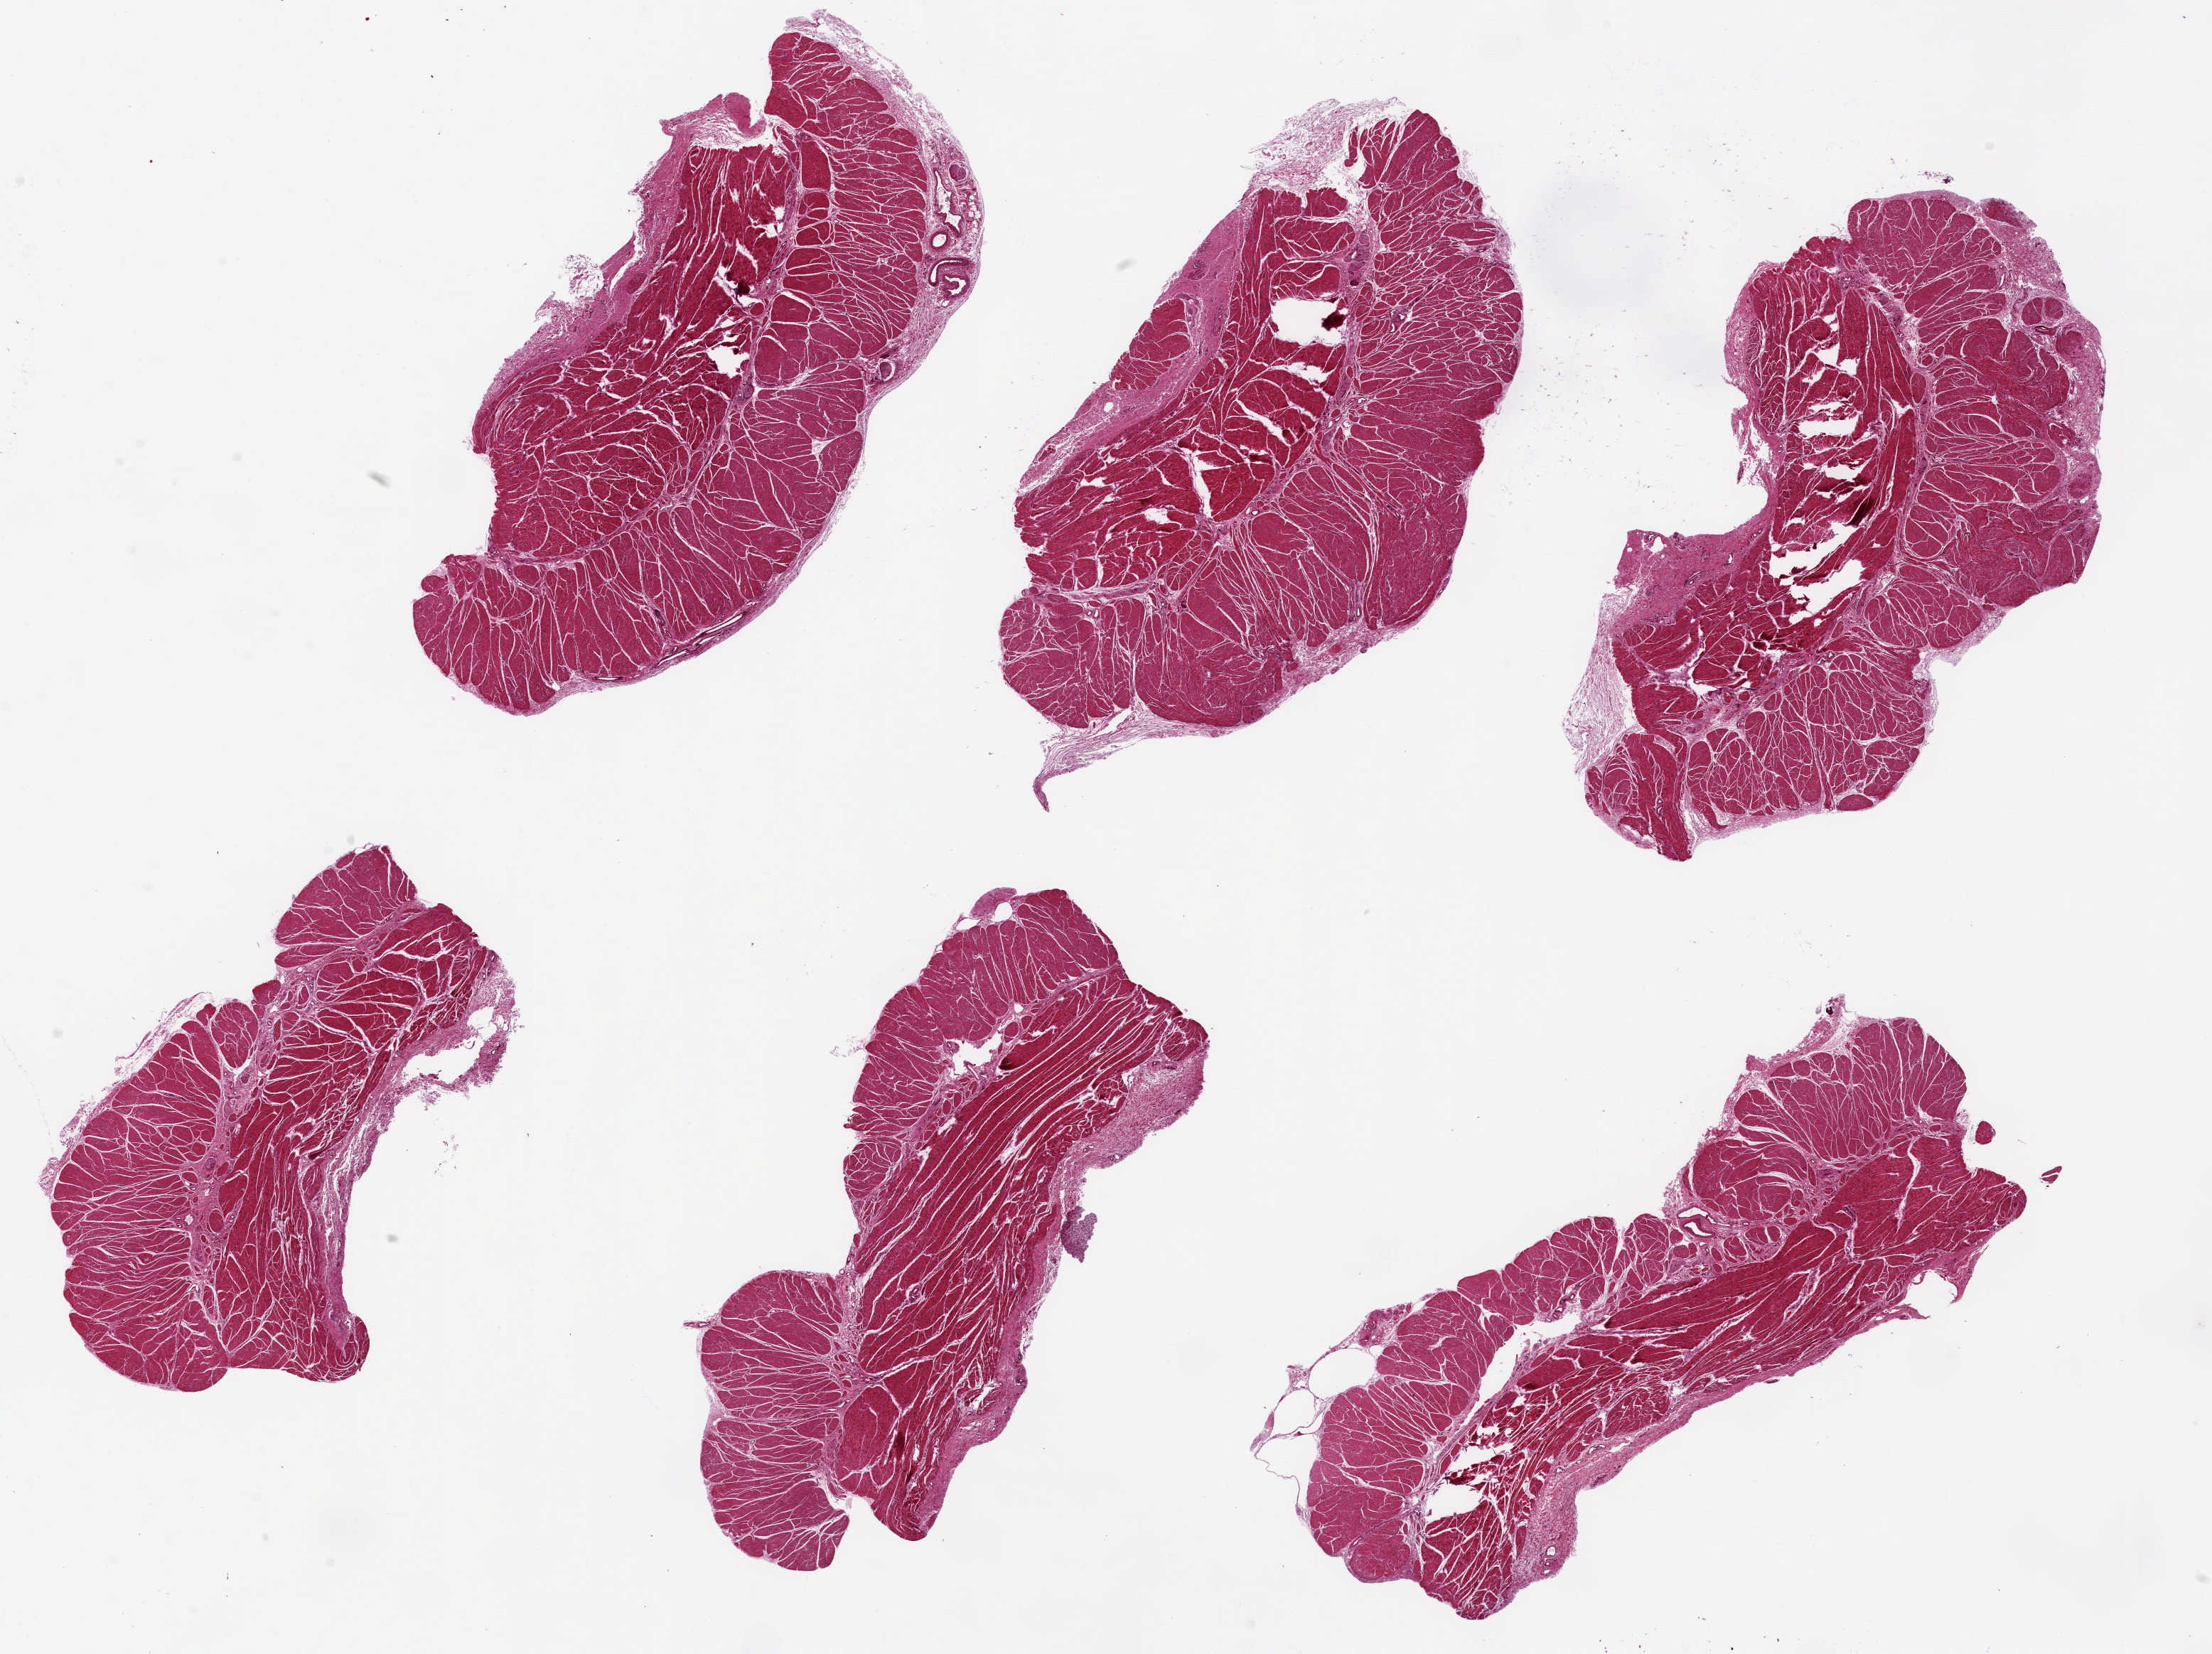
Digitized hematoxylin and eosin (H&E)-stained section, brightfield, a low-resolution overview of the entire scanned area, about 24.6 x 18.4 mm, PAXgene-fixed paraffin-embedded (PFPE) section, target tissue: esophageal muscle, tissue donor sample. Donor: male.
Pathologist's review note for this sample: 6 pieces ~7x4mm.